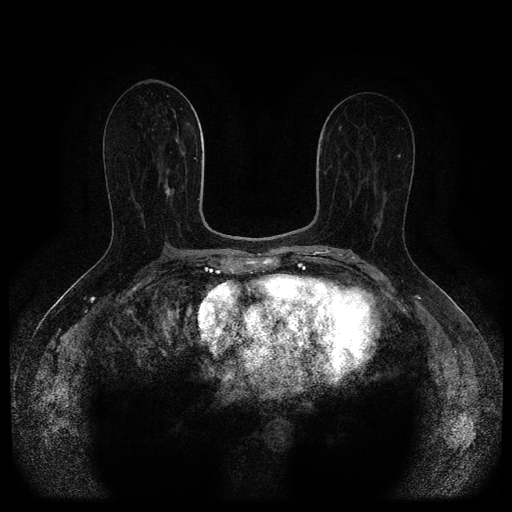
Breast MRI (dynamic contrast-enhanced, multi-phase), one axial slice; slice 53 of 116 in the series (ordered by position); dynamic contrast-enhanced series, time point 2 of 5 at this slice position (early post-contrast); 1.5 T; TE 2.7 ms, TR 5.4 ms; 2 mm slice thickness; 512 × 512 image matrix, field of view 340 × 340 mm. Female patient, age 71 years.
Annotated regions visible in this slice (semi-automatic segmentation, software-assisted and operator-edited):
- breast lesion (labelled 'tumour' in the annotation; benign lesions carry a separate 'benign' label): bounding box (x1, y1, x2, y2) in pixels: (164, 183, 174, 198)